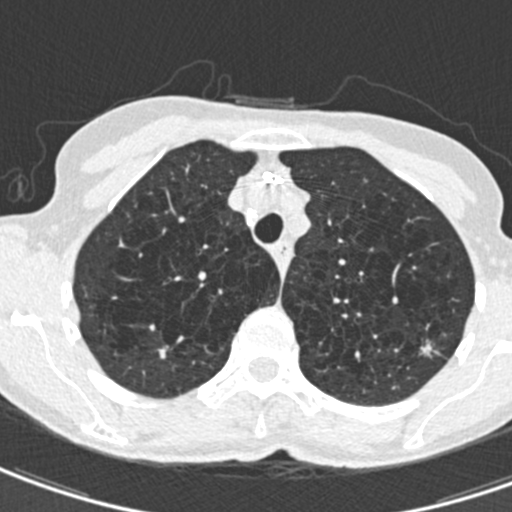
Low-dose screening chest CT, axial slice, second screening round (one year after baseline), lung window (W 1500 / L -600 HU), slice 119 of 498 in the series. Female participant, aged 71 years at enrolment. Current smoker at enrolment.
- Lesion marked by an expert reader, bounding box [x1, y1, x2, y2] px = [404, 331, 444, 369].
- The screening reader recorded 2 non-calcified nodules or masses ≥4 mm on this exam; which of them this box marks is not recorded.
- Later outcome: lung cancer diagnosed 604 days after this screen — adenocarcinoma, NOS, left upper lobe, moderately differentiated (G2), stage IA (AJCC 6th edition), 12 mm at pathology.